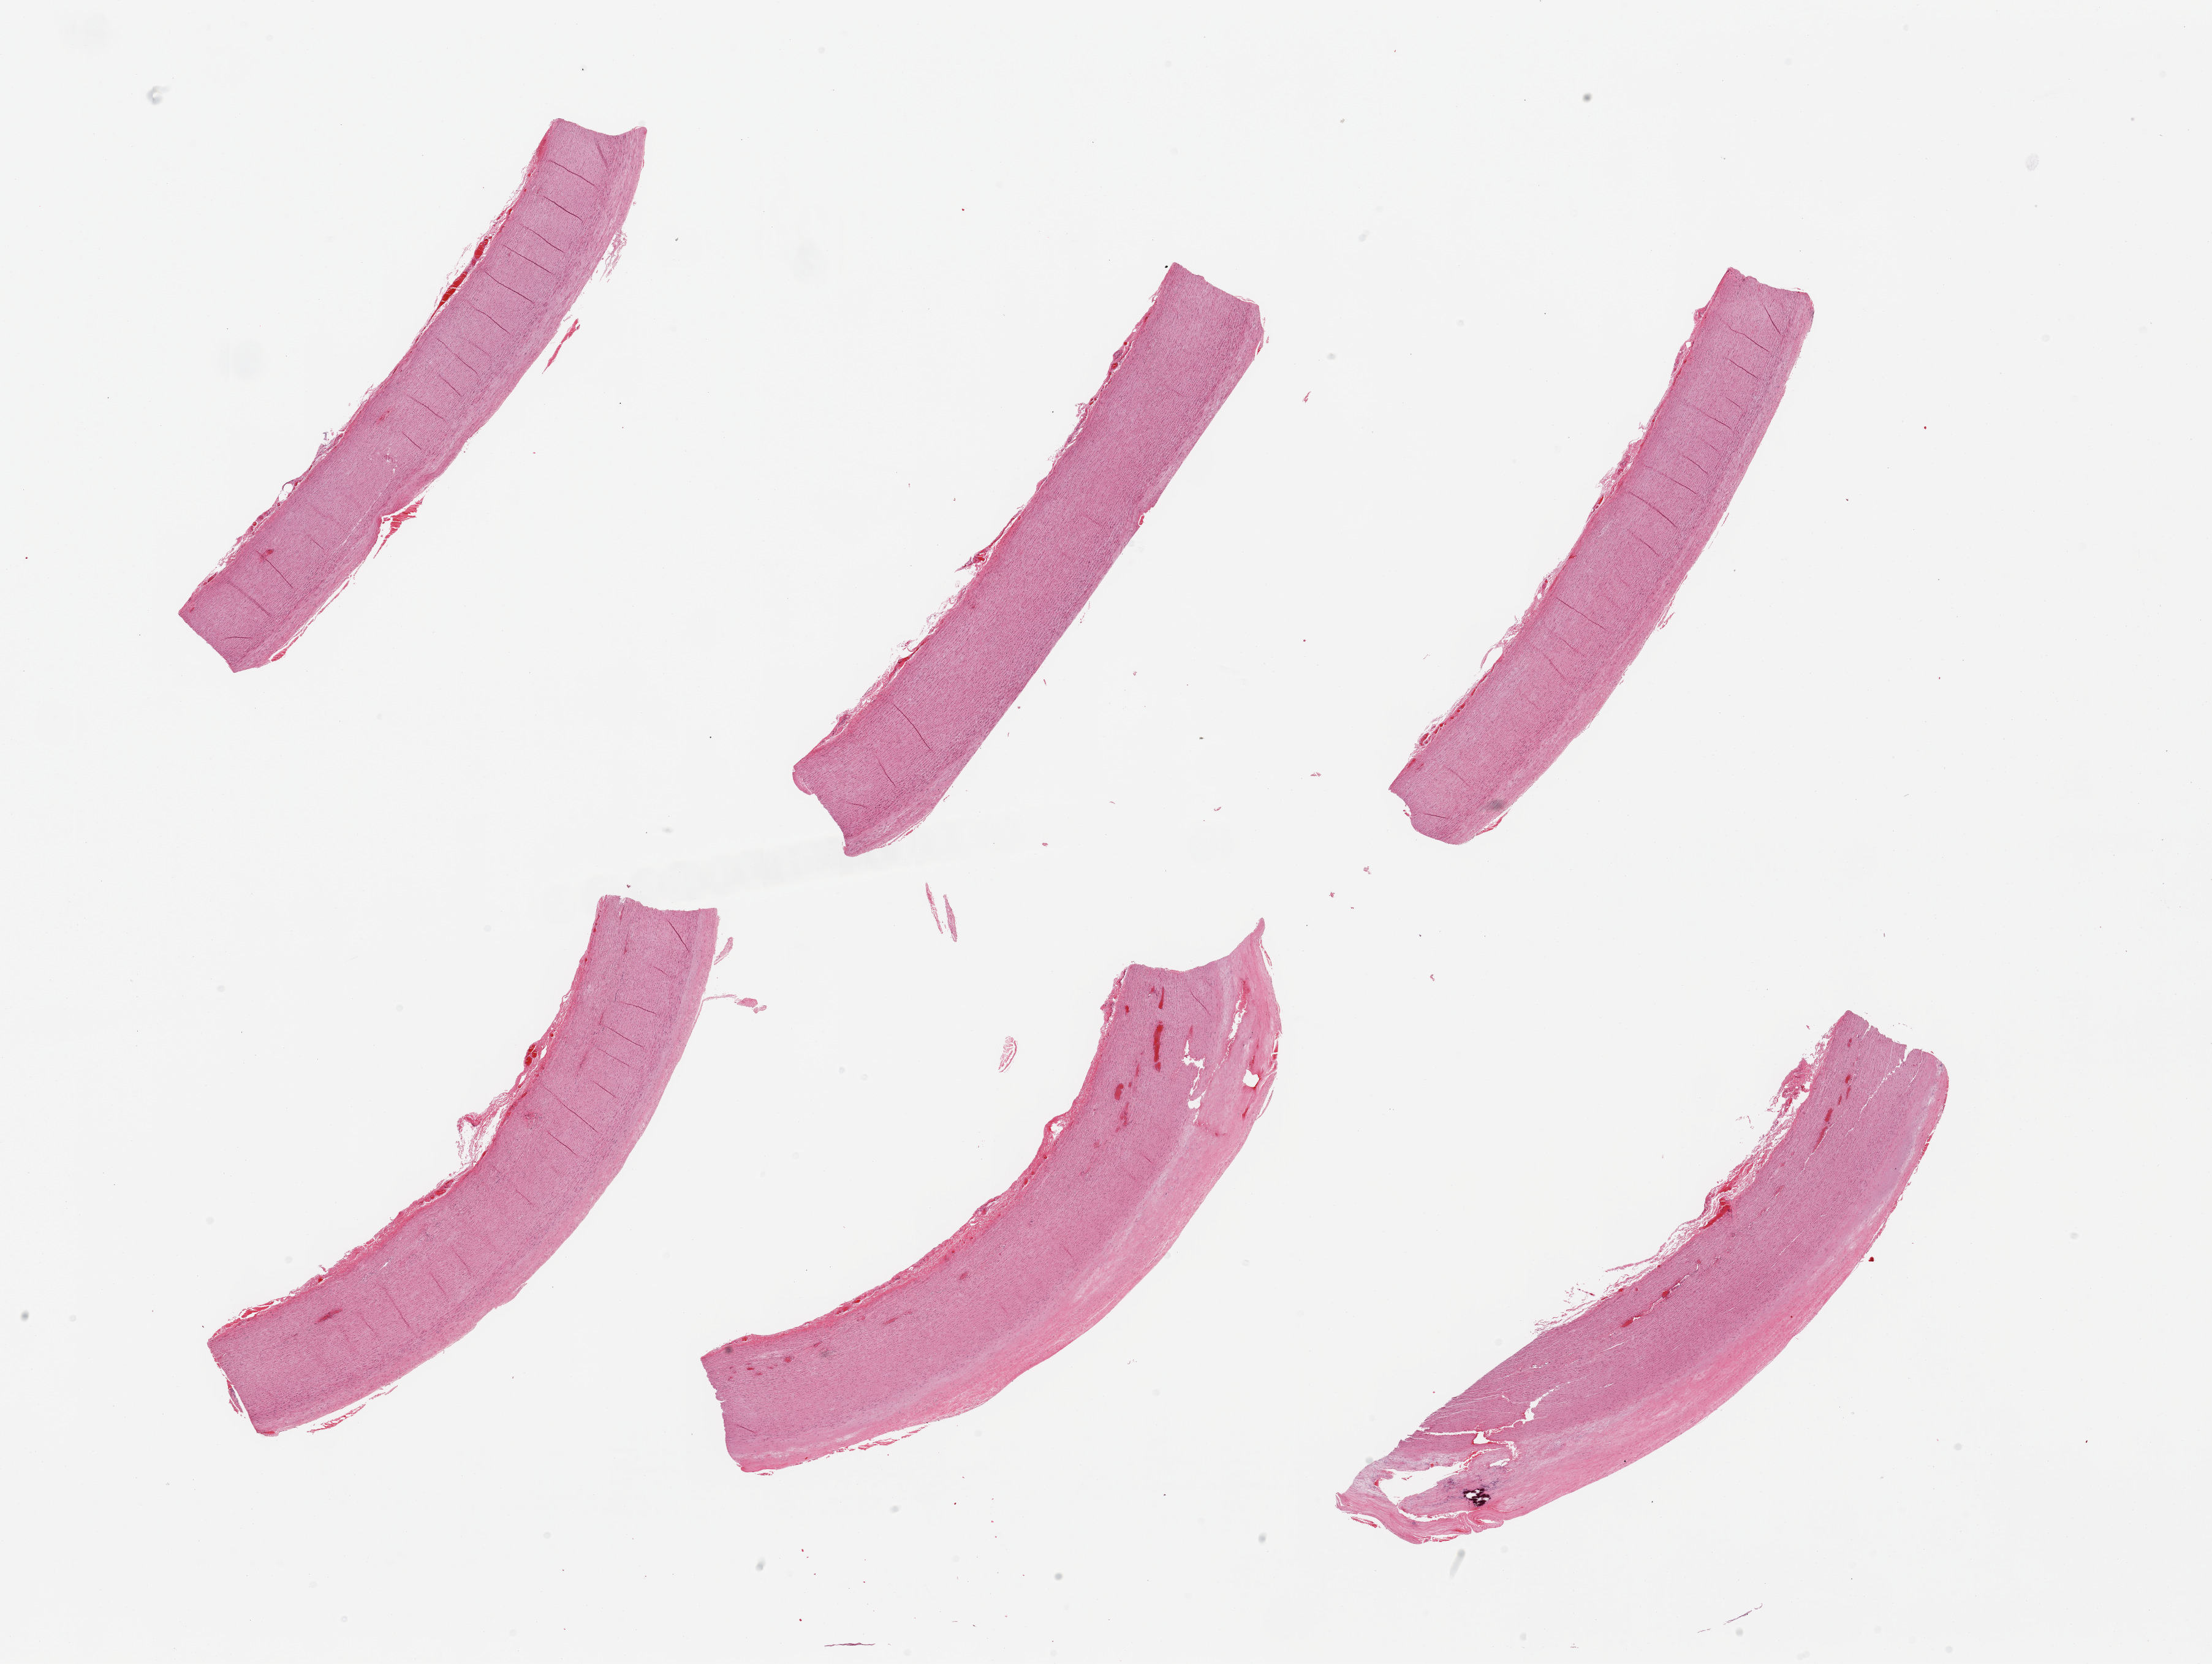
Whole-slide image, haematoxylin and eosin stain, a low-resolution overview of the entire scanned area, about 28.5 x 21.5 mm. PAXgene-fixed, paraffin-embedded tissue. Sampled site (target tissue): aorta. Donor tissue sample. Donor sex: male.
Pathologist's review note for this sample: 6 pieces, atherosis up to ~1mm.